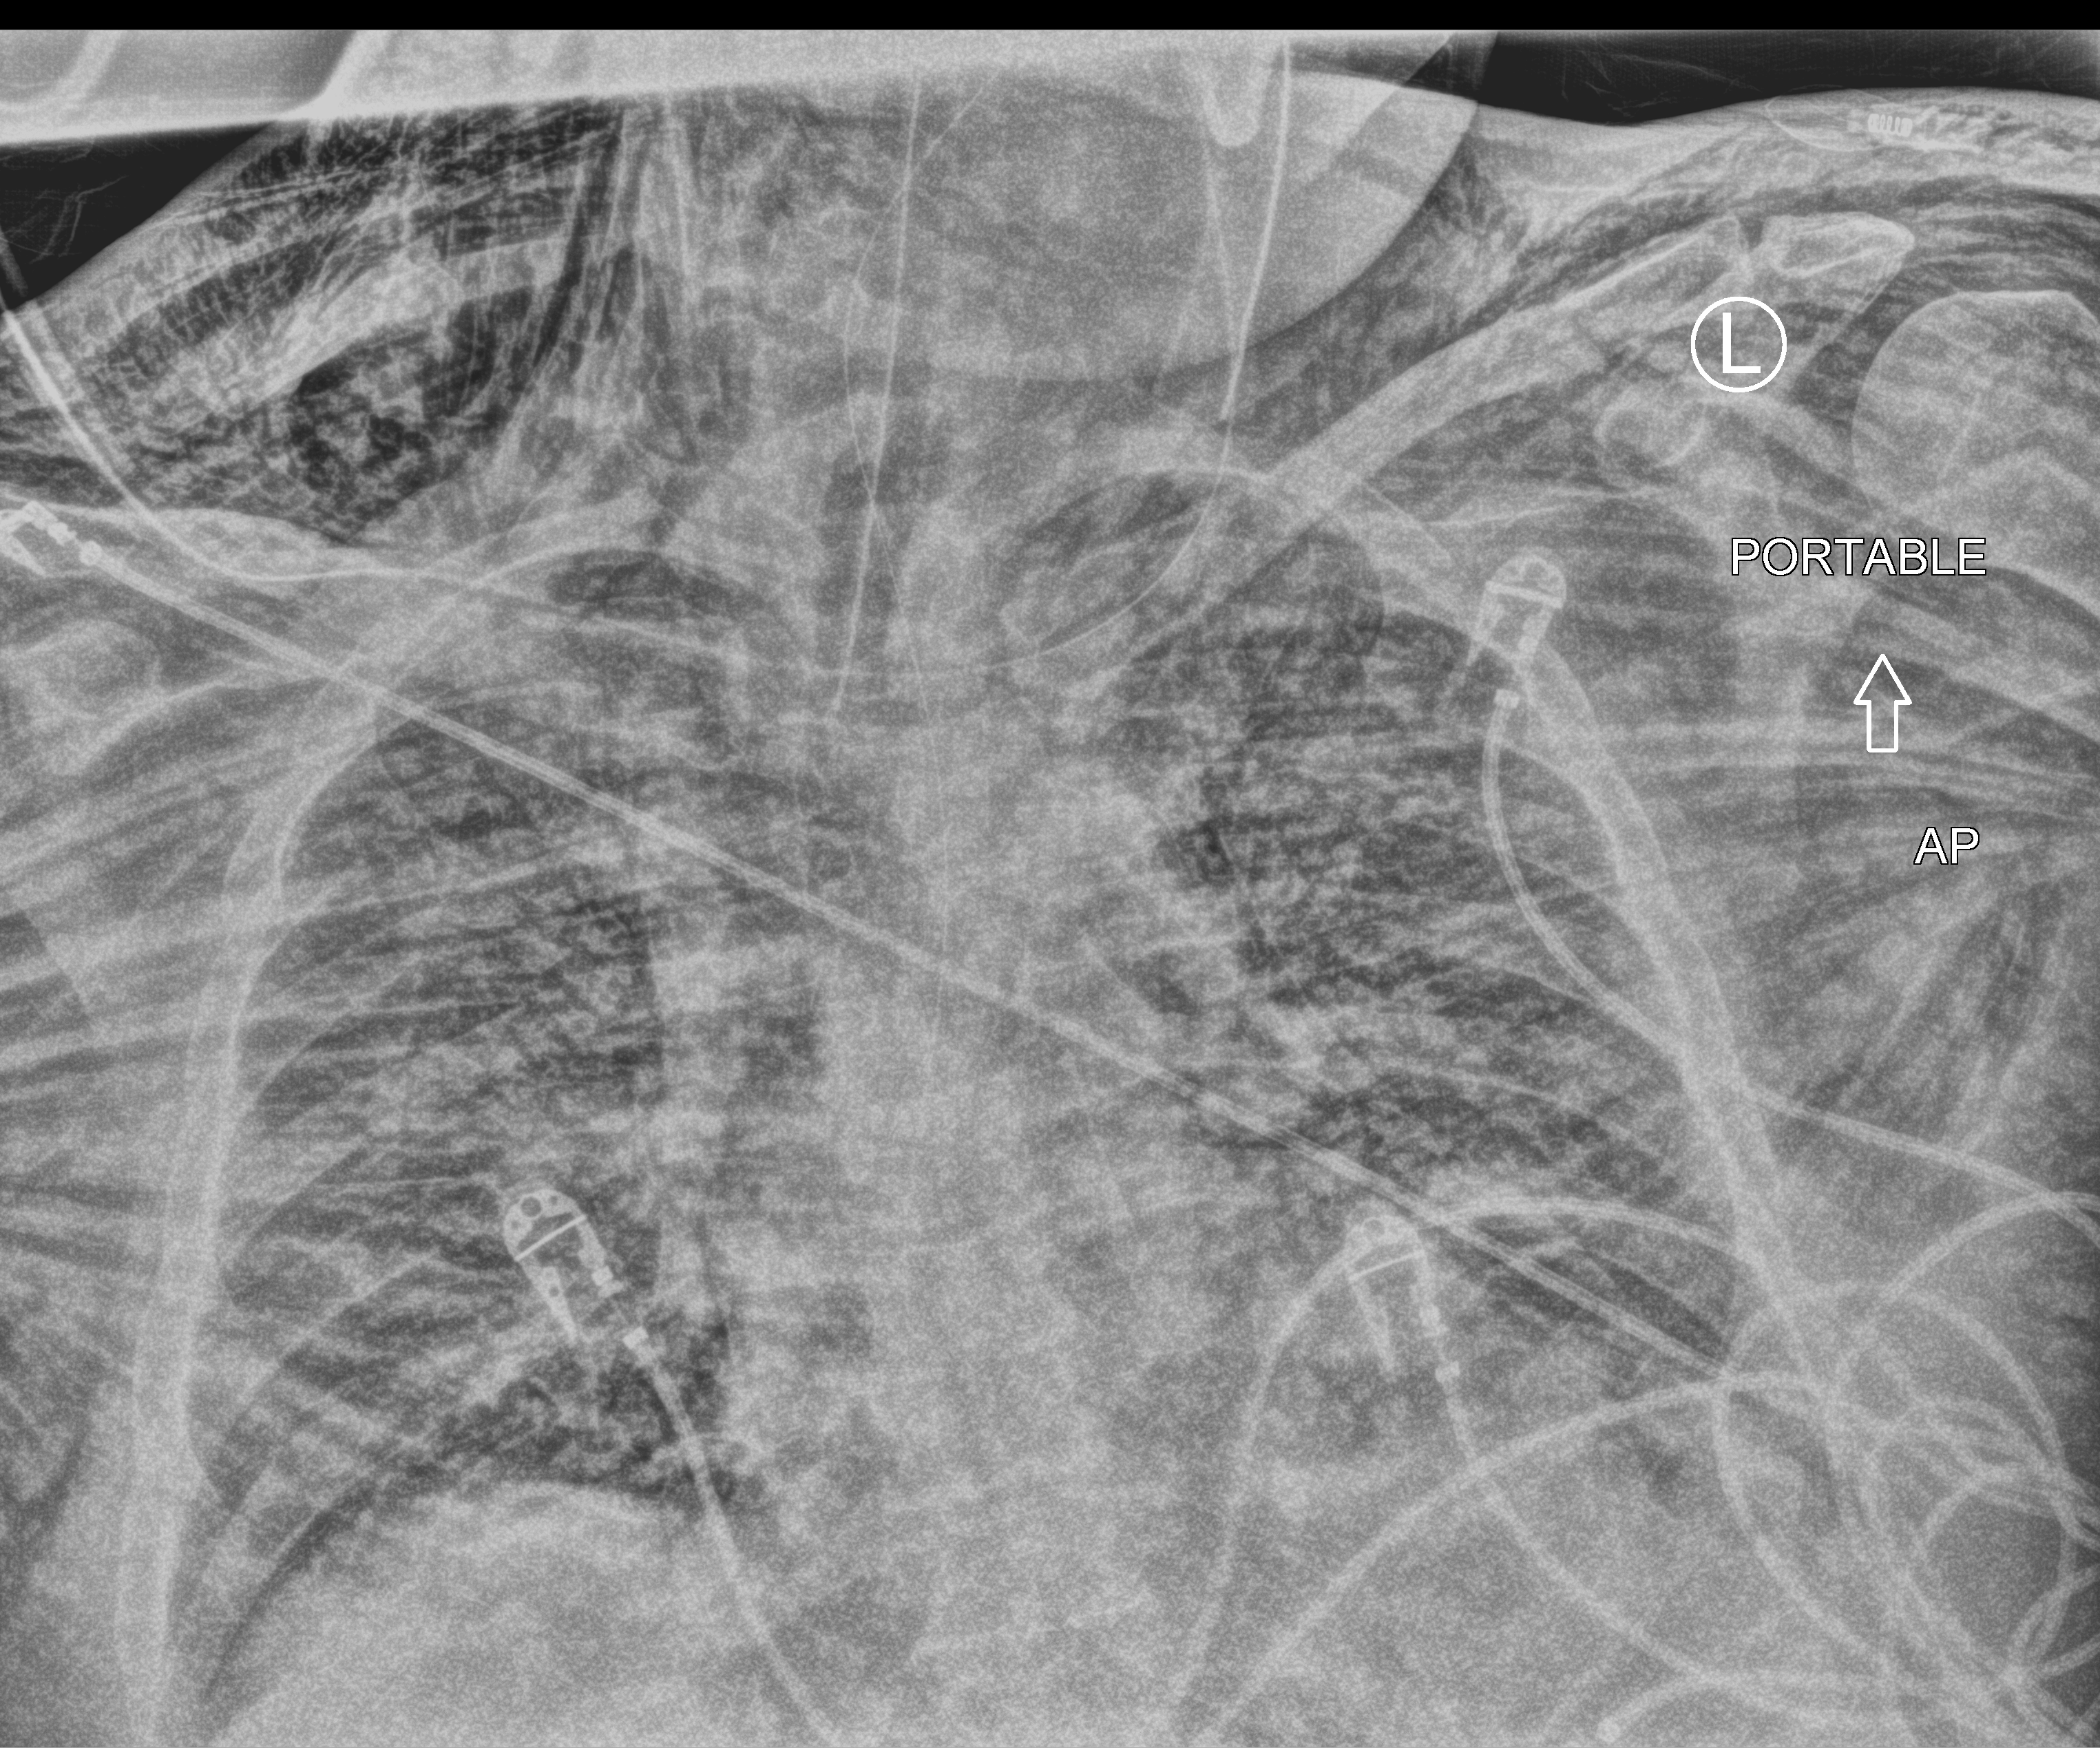
Portable chest radiograph. Patient hospitalised with COVID-19, aged 18–59 years.
From the hospital-stay record, not from the radiograph (when in the stay this image was taken is not recorded):
- length of hospital stay: 26 days
- mechanically ventilated during this hospital stay: yes